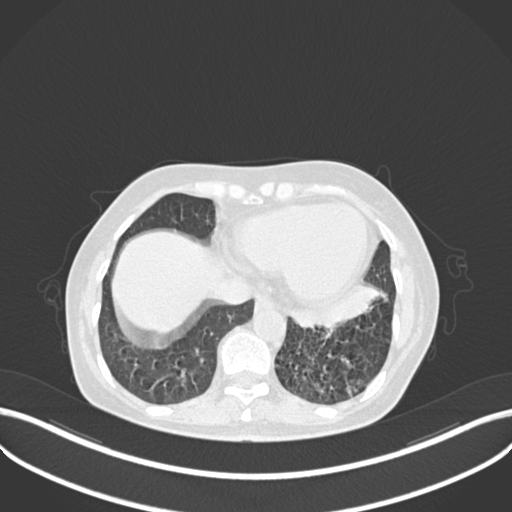
Chest CT, one axial slice; position 69 of 270 along the scan axis; reconstruction kernel B30f; 120 kVp; lung window (W 1500 / L -600 HU); 512 × 512 image matrix, field of view 400 × 400 mm. Patient: female, 63 years. From the clinical record (not read from this slice): clinical TNM (as recorded): T1b N0 M0; histopathological grade: G2-3.
Outlined on this slice (bounding box drawn by a radiologist):
- lung tumour (recorded histology: adenocarcinoma): bounding box [x1, y1, x2, y2] px = [288, 276, 387, 334]